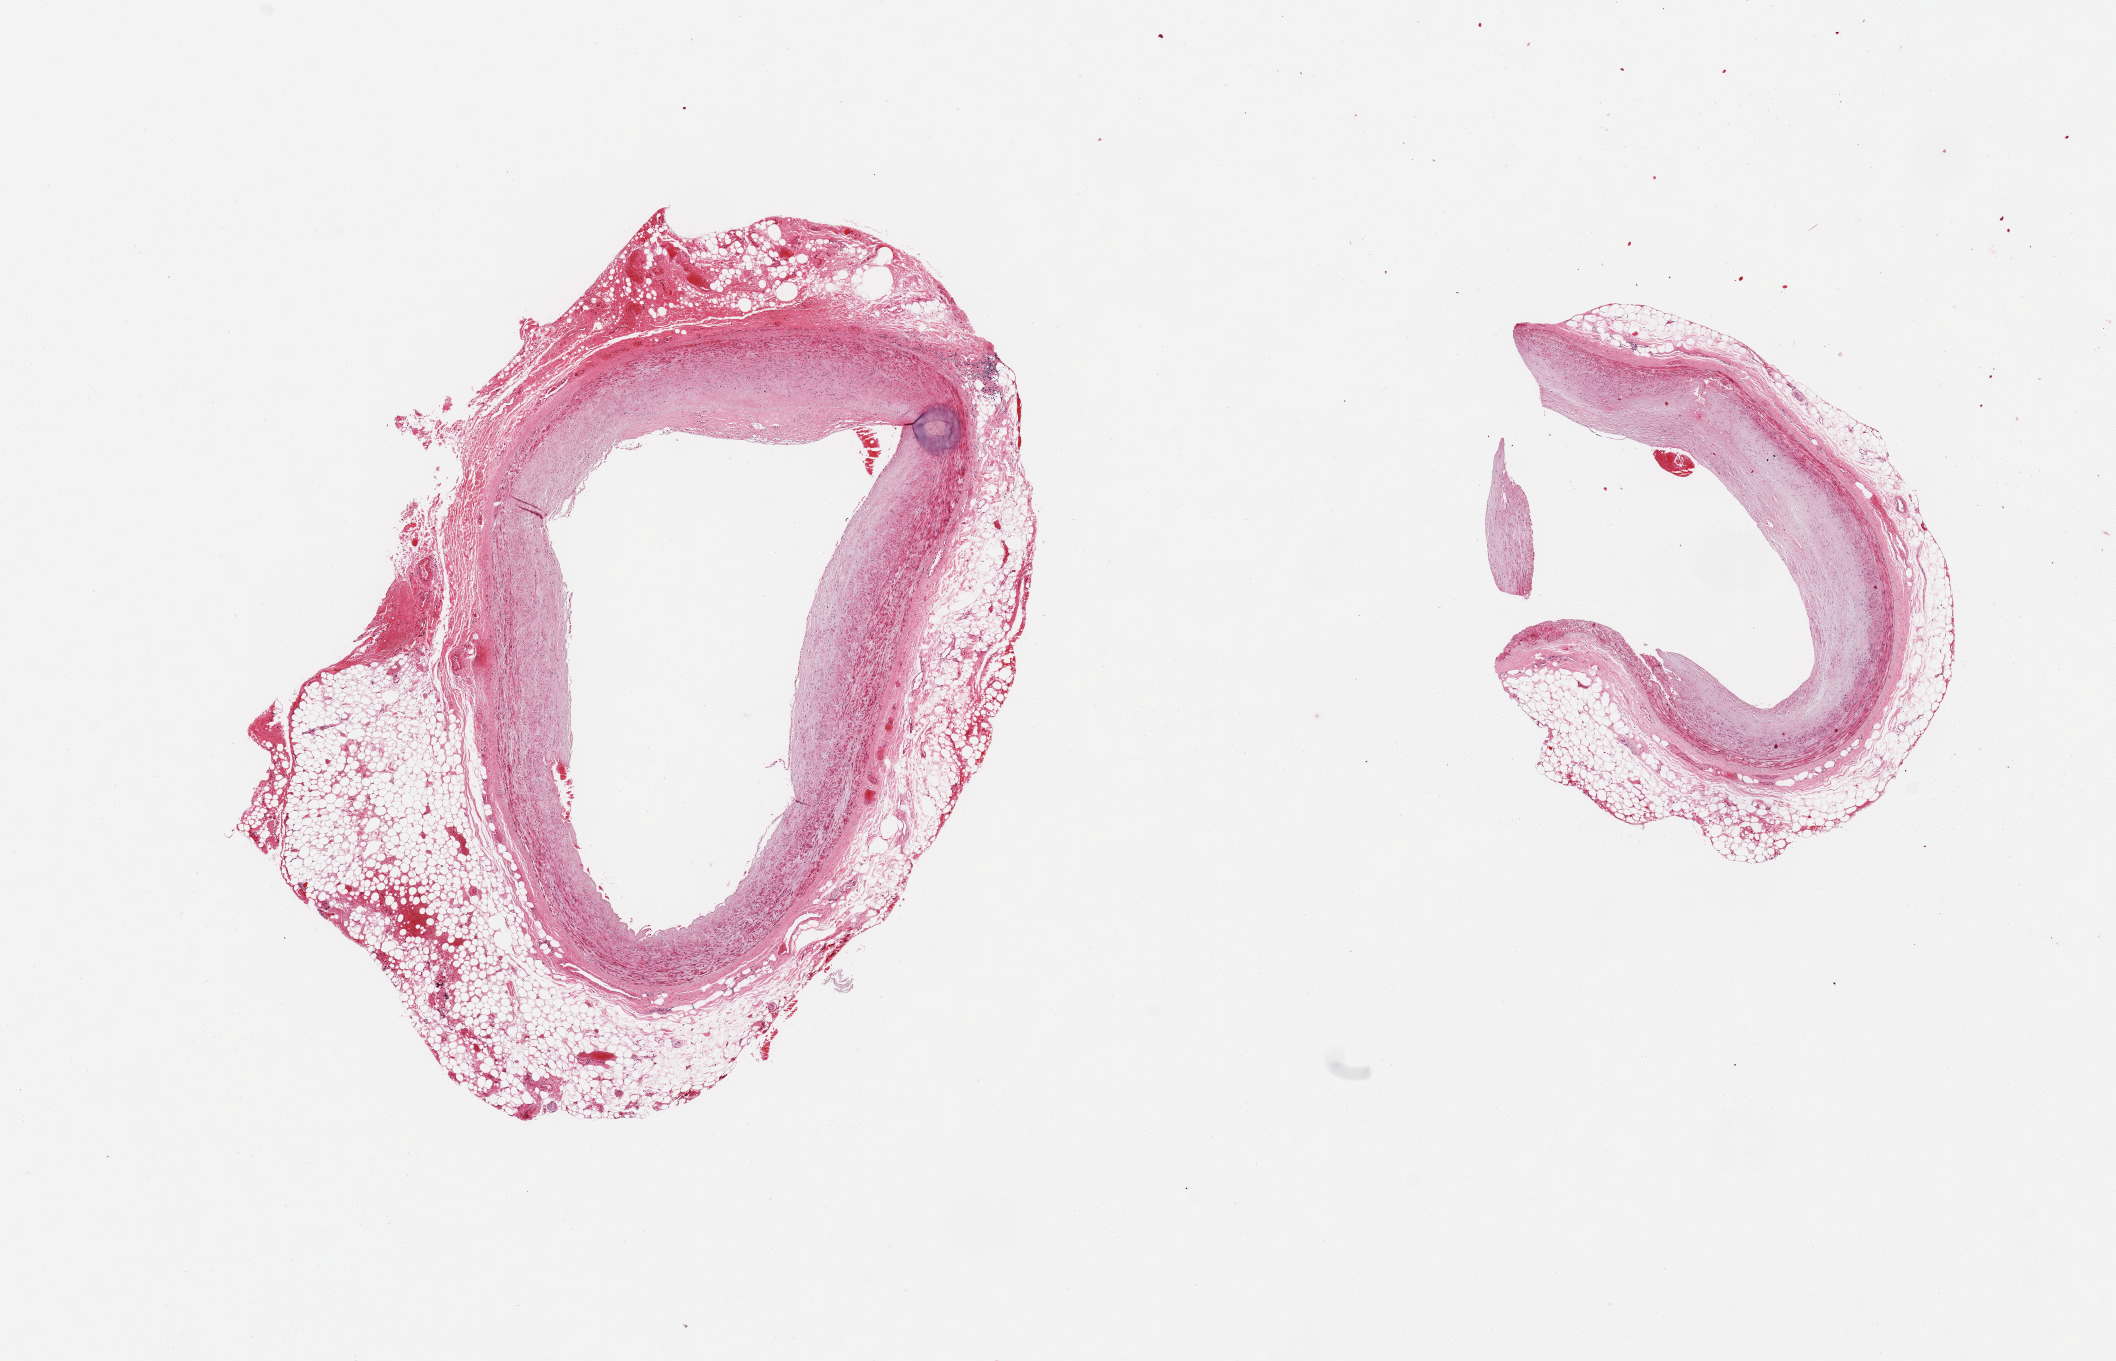
Haematoxylin and eosin whole-slide image, brightfield — shown as a low-resolution overview of the whole scanned area (about 16.7 x 10.8 mm), PAXgene-fixed paraffin-embedded (PFPE) section, sampled site (target tissue): coronary artery, donor tissue sample. Donor: male.
Reviewer comment on this tissue sample: 2 pieces; atherosclerosis, ~50% is attached fat.